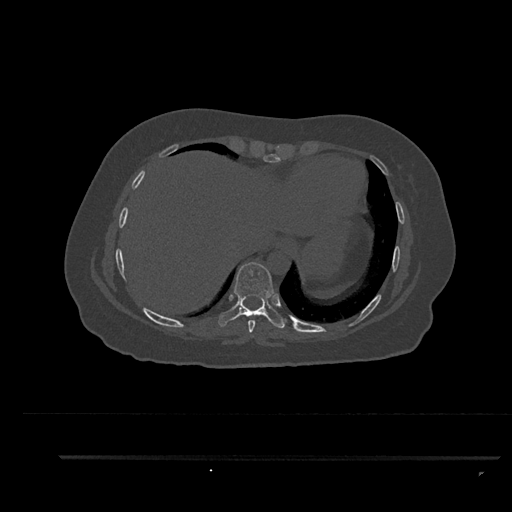
CT including the spine, one axial slice. Slice 424 of 797 in the series (ordered by position). Reconstruction kernel Br40s/3. 120 kVp. Bone window (W 1800 / L 400 HU). 0.5 mm slice thickness. 512 × 512 image matrix, field of view 408 × 408 mm. Female patient, age 44 years. Case-level facts recorded for this patient, not image findings: primary cancer: renal; vertebrae with lytic lesions (as recorded): L1.
Annotated regions visible in this slice (semi-automatic segmentation, software-assisted and operator-edited):
- T8 vertebra: box from (x=248, y=314) to (x=256, y=333) px
- T9 vertebra: (x=218, y=262)–(x=286, y=329)